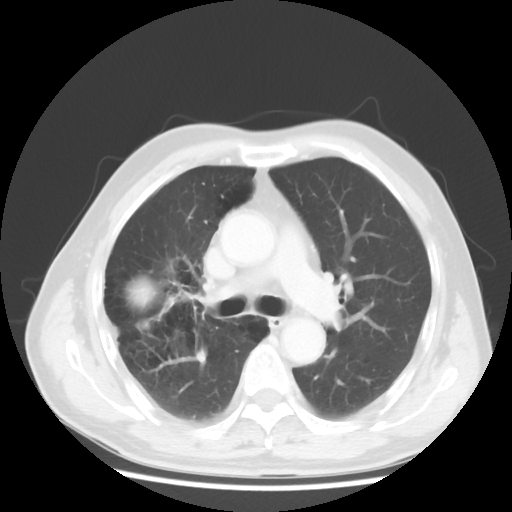
Chest CT, one axial slice; position 30 of 50 along the scan axis; reconstruction kernel STANDARD; 120 kVp; lung window (W 1500 / L -600 HU); 5 mm slice thickness; 512 × 512 image matrix, field of view 360 × 360 mm. Male patient, age 69 years. Case-level facts recorded for this patient, not image findings: clinical TNM (as recorded): T3 N0 M0; histopathological grade: G3.
Annotated regions visible in this slice (rectangle marked by the reading radiologist):
- lung tumour (recorded histology: adenocarcinoma): bounding box (x1, y1, x2, y2) in pixels: (123, 271, 163, 317)